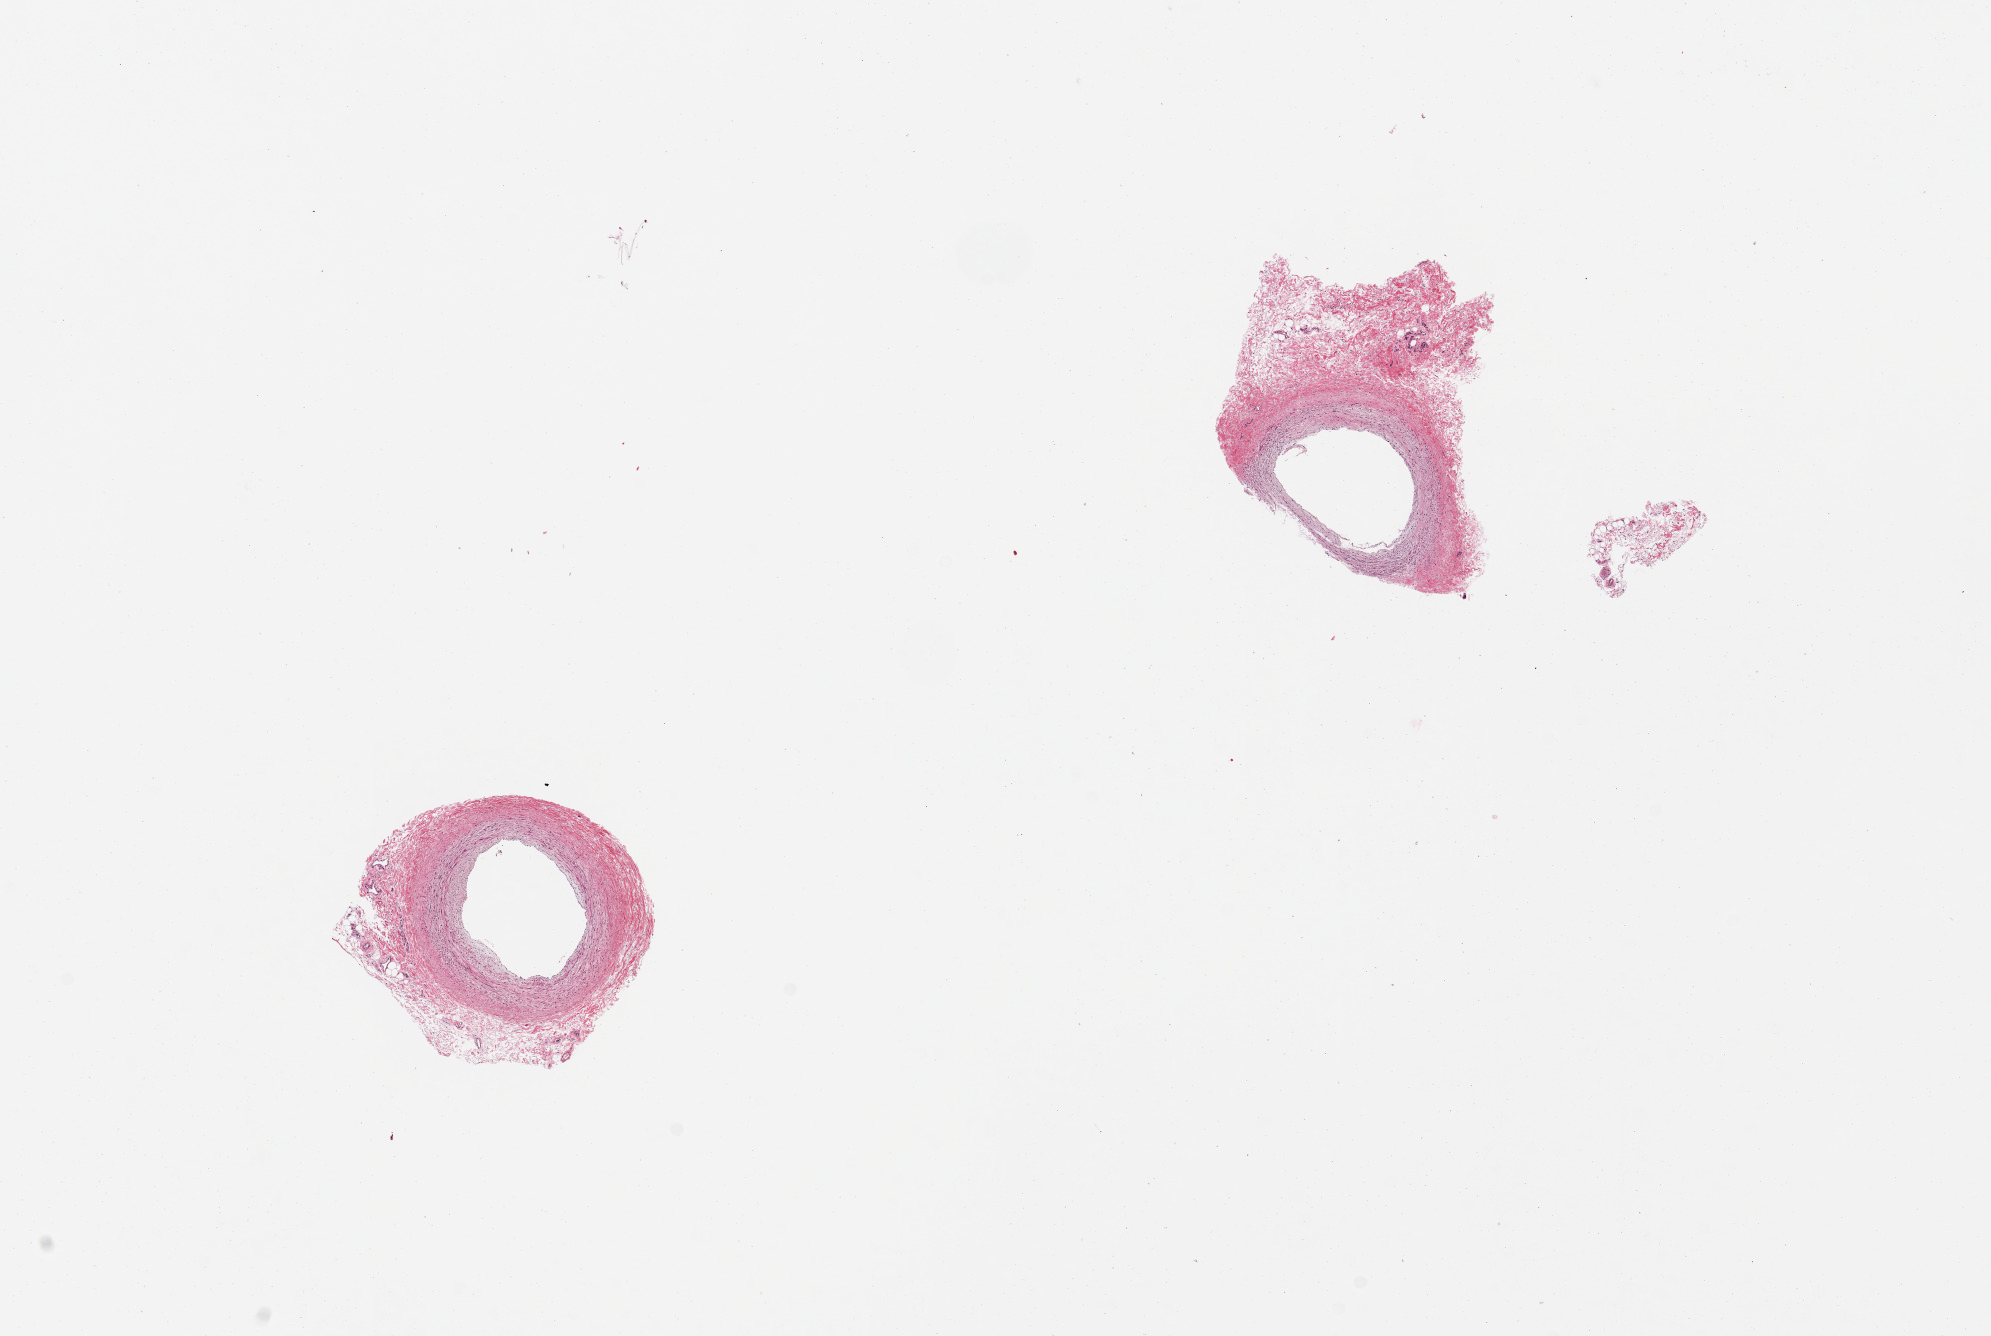
Digitized H&E-stained section, whole scanned area (about 15.8 x 10.6 mm, slide scanned at 20x) shown as a low-resolution overview; PAXgene-fixed paraffin-embedded (PFPE) section; sampled site (target tissue): coronary artery; donor tissue sample. Donor: female.
* review note (as recorded): 2 pieces, adherent fat/fibrous tissue, up to ~0.7mm on both; Minimal atherosis